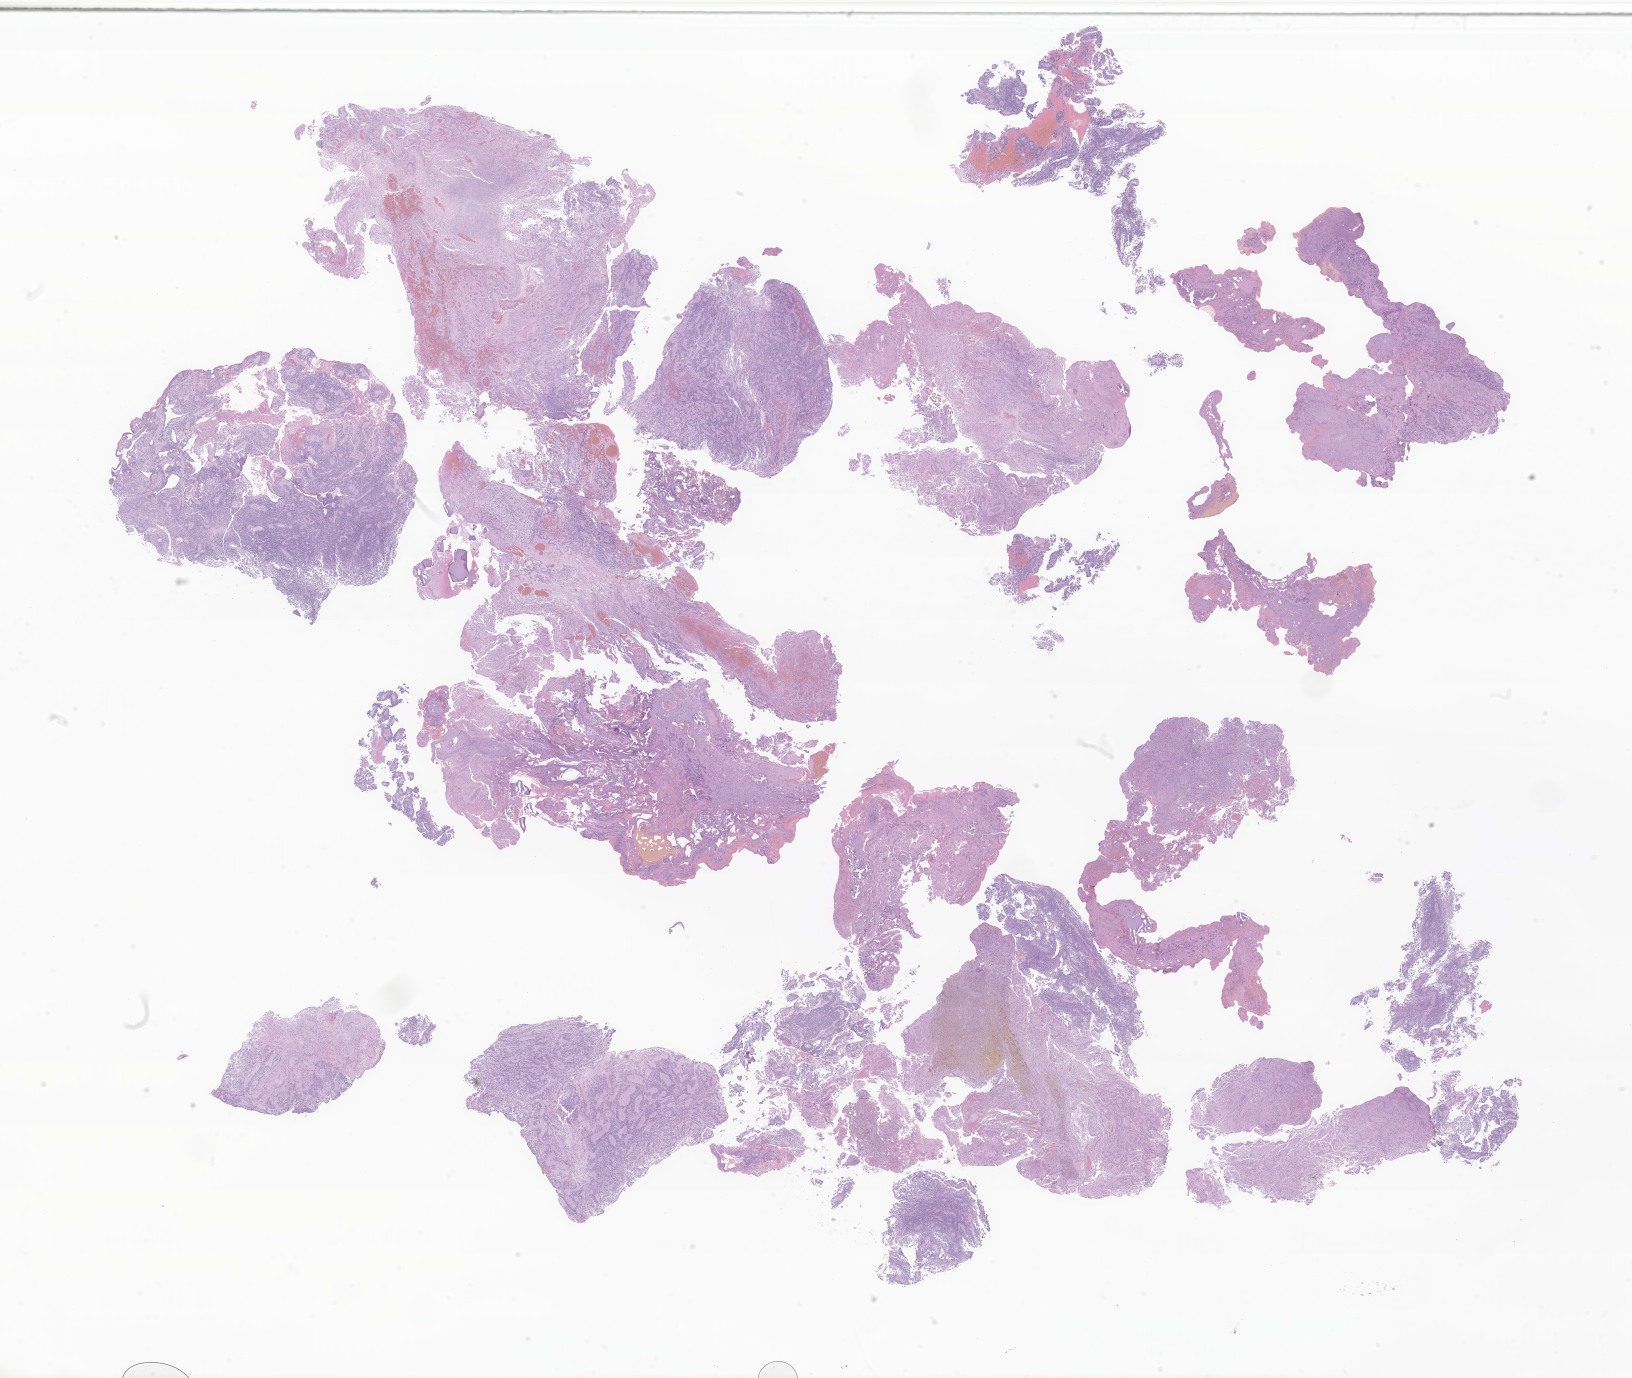
Whole-slide image, H&E stain of tumor tissue from the cerebral ventricle, shown as a low-resolution overview of the whole scanned area (about 27.5 x 23.2 mm); FFPE section. Male patient, age 106 months (8 years 10 months).
* diagnosis: Ependymoma, NOS